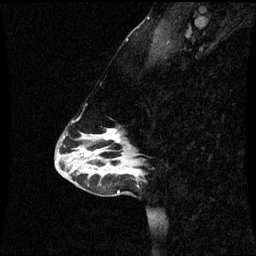
Breast MRI (dynamic contrast-enhanced), one sagittal slice; slice 22 of 60 in the series (ordered by position); dynamic contrast-enhanced series, image 2 of 3 at this slice position (ordered by acquisition); 1.5 T; TE 4.2 ms, TR 8.9 ms; 256 × 256 image matrix, field of view 220 × 220 mm. Female patient, age 43 years. From the clinical record (not read from this slice): setting: breast cancer imaged before/during neoadjuvant chemotherapy; receptor status: HR-positive, HER2-negative.
Annotated regions visible in this slice (semi-automatic segmentation, software-assisted and operator-edited):
- analysis volume of interest (the breast-tissue region the enhancement analysis was run in; not a lesion): bounding box <84,130,142,171> (left, top, right, bottom; pixels)
- tumour enhancement mask (voxels above the 70 % enhancement threshold inside the analysis volume of interest): <103,130,120,143>